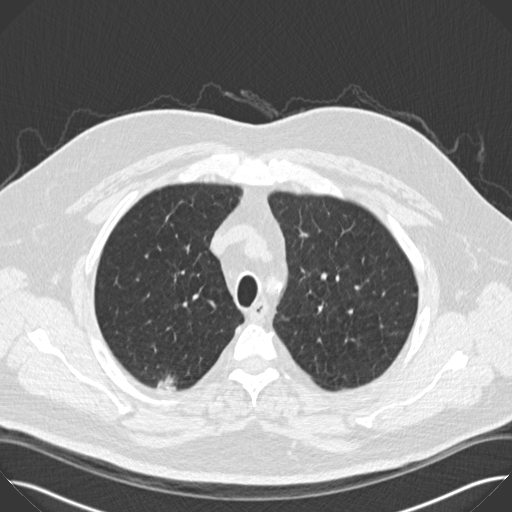
Low-dose screening chest CT, axial slice, baseline screening round, lung window (W 1500 / L -600 HU), 2 mm slice thickness, slice 126 of 158 in the series. Male, age 65 years at enrolment. Former smoker at enrolment.
Lesion marked by an expert reader, bounding box (x1, y1, x2, y2) in pixels: (148, 359, 192, 415). The screening reader recorded 2 non-calcified nodules or masses ≥4 mm on this exam (right upper lobe, right upper lobe); which of them this box marks is not recorded. Participant outcome: lung cancer diagnosed 47 days after this screen — bronchiolo-alveolar adenocarcinoma, NOS, right upper lobe, moderately differentiated (G2), stage IIA (AJCC 6th edition), 14 mm at pathology.